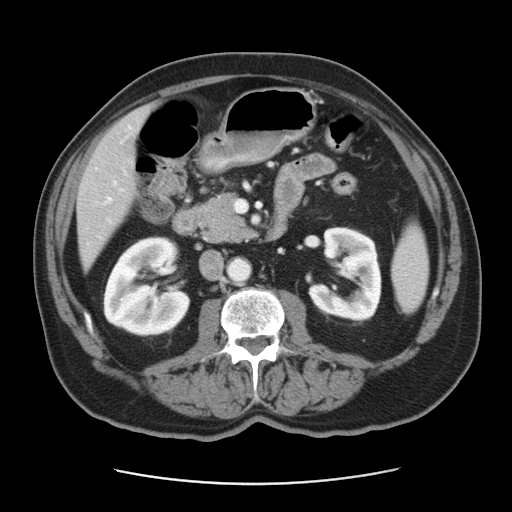
Contrast-enhanced abdominal CT, one axial slice. Slice 17 of 42 in the series (ordered by position). Intravenous contrast given. Soft-tissue window (W 400 / L 40 HU). 5 mm slice thickness. 512 × 512 image matrix. Male patient, age 73 years. From the clinical record (not read from this slice): diagnosis: colorectal cancer liver metastases, imaged before liver resection; multiple liver metastases: yes; largest metastasis: 0.5 cm; disease in both lobes: no.
Structures marked on this image (outlined manually by an expert reader):
- hepatic veins: bounding box <104,182,117,204> (left, top, right, bottom; pixels)
- liver: <78,108,151,268>
- planned liver remnant (the part of the liver to remain after resection): <109,109,151,154>